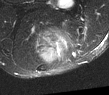
MRI of an extremity soft-tissue mass, one axial slice; slice 38 of 52 in the series (ordered by position); T2-weighted fat-saturated; MR volume resampled by the dataset authors to the PET/CT grid (not the native acquisition matrix); 3.27 mm slice thickness; 109 × 95 image matrix, field of view 106 × 93 mm. Male patient. From the clinical record (not read from this slice): histological type: synovial sarcoma; site of the primary tumour: left poplietal fossa.
Structures marked on this image (expert contour drawn on MRI and transferred to this co-registered scan by the dataset authors):
- gross tumour volume (mass): bounding box (x1, y1, x2, y2) in pixels: (35, 29, 64, 64)